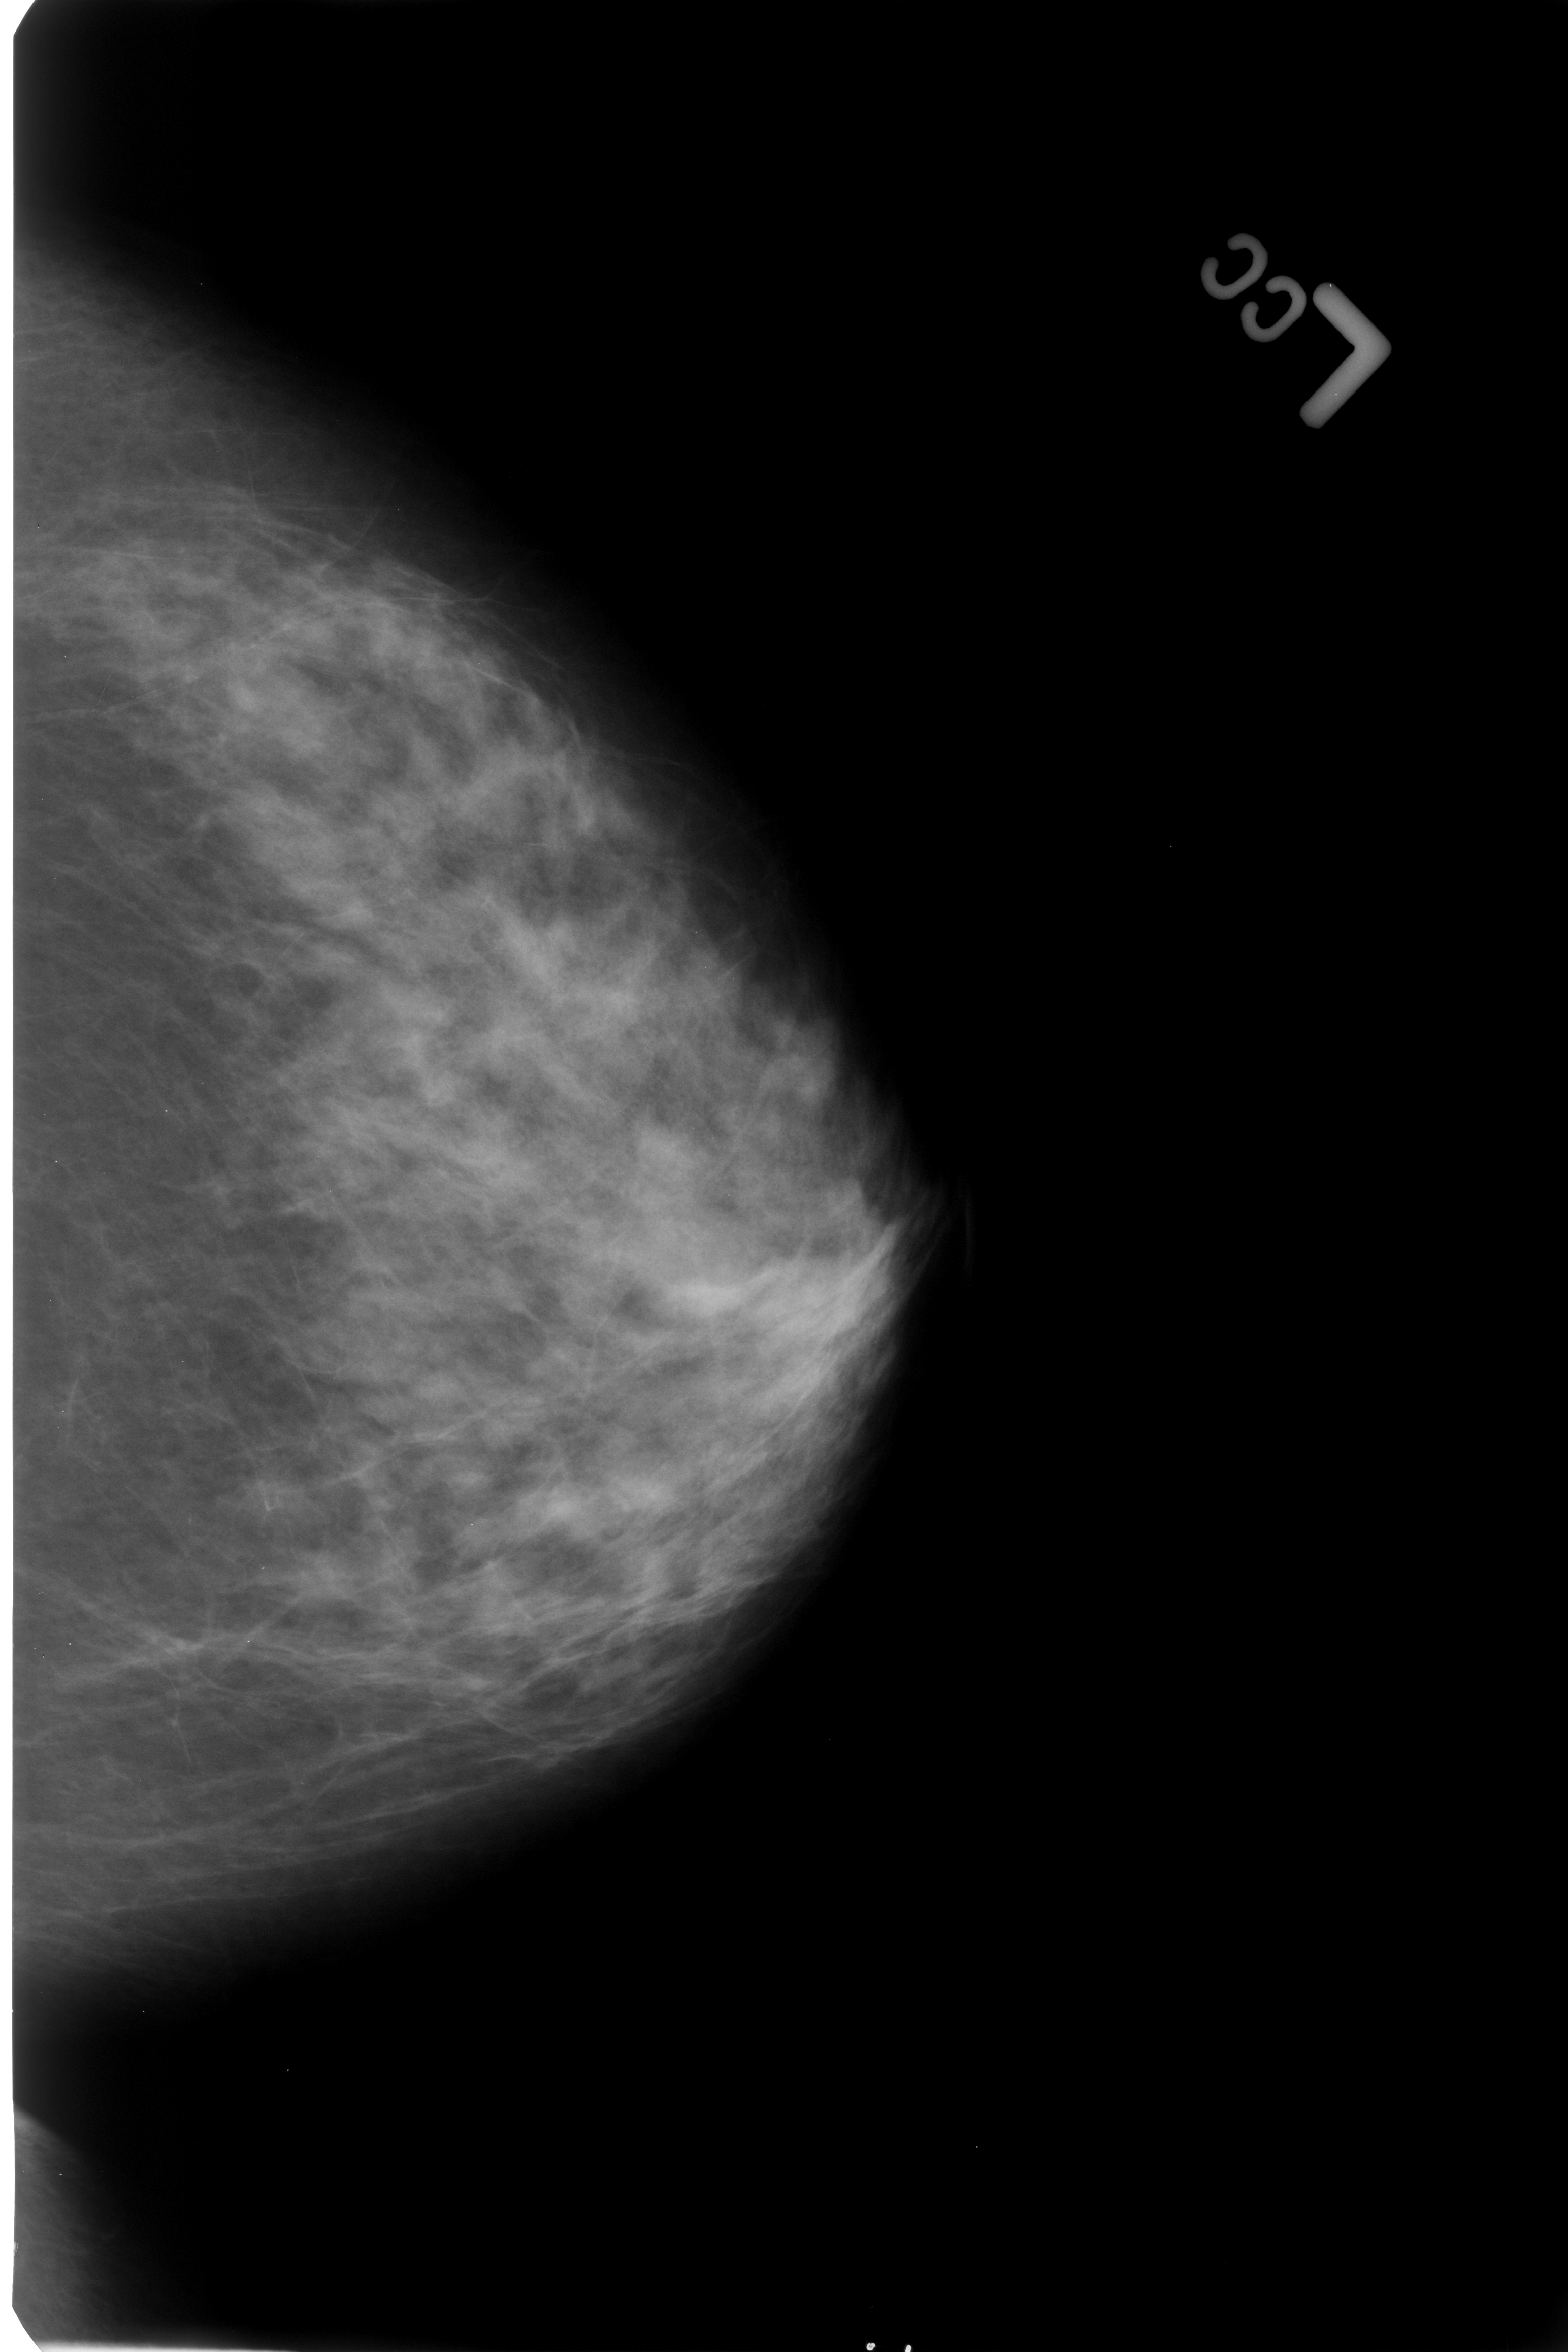
Mammogram (digitized film); left breast; CC view; BI-RADS breast density category 3 (scale 1–4).
- Finding: calcifications, morphology vascular; BI-RADS assessment category 2; subtlety rating 3 on a 1 (subtle) to 5 (obvious) scale; benign without callback (not worked up further).